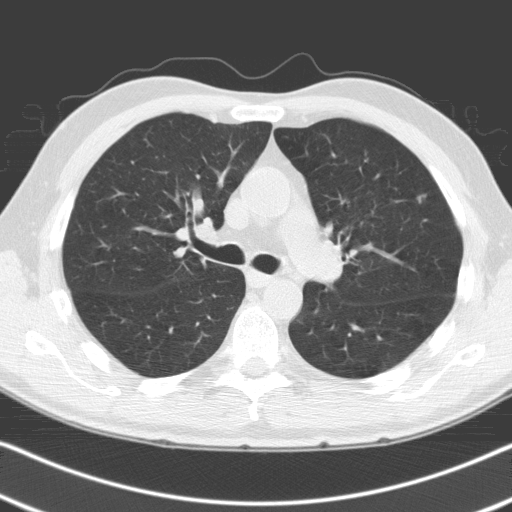
Chest CT (low-dose screening protocol), one axial image, second annual screen, lung window (W 1500 / L -600 HU), standard (soft-tissue) reconstruction kernel (C), 120 kVp, slice 62 of 163 in the series, 512 × 512 image matrix. Male participant, aged 68 years at enrolment.
• Lesion marked by an expert reader, bounding box <398,181,443,223> (left, top, right, bottom; pixels).
• No non-calcified nodule or mass ≥4 mm was recorded by the screening reader at this exam.
• Official screen result: negative screen, no significant abnormalities.
• Lung cancer was diagnosed 685 days after this screen (after the third annual screen): adenocarcinoma, NOS, left upper lobe, moderately differentiated (G2), stage IA (AJCC 6th edition), 6 mm at pathology.